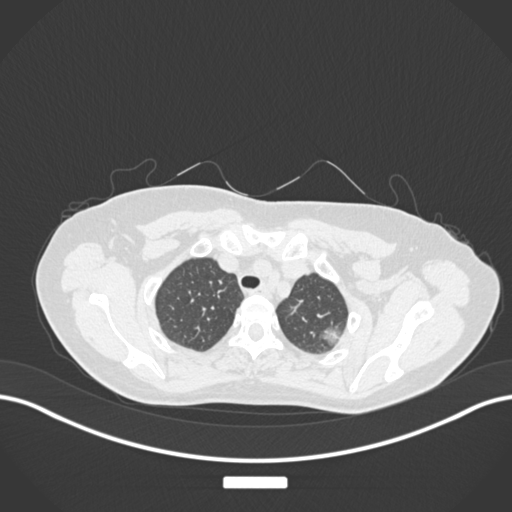
Chest CT, one axial slice. Position 146 of 181 along the scan axis. 120 kVp. Lung window (W 1500 / L -600 HU). 1 mm slice thickness. 512 × 512 image matrix. Patient: female, 58 years. Case-level facts recorded for this patient, not image findings: clinical TNM (as recorded): T1c N0 M0.
Annotated regions visible in this slice (rectangle marked by the reading radiologist):
- lung tumour (recorded histology: adenocarcinoma): bounding box (x1, y1, x2, y2) in pixels: (317, 318, 342, 350)